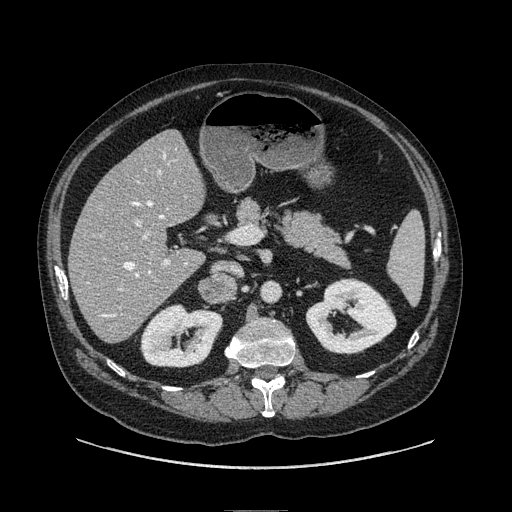
Contrast-enhanced abdominal CT, one axial slice. Slice 36 of 149 in the series (ordered by position). Soft-tissue window (W 400 / L 40 HU). 1.25 mm slice thickness. 512 × 512 image matrix. Male patient. Case-level facts recorded for this patient, not image findings: diagnosis: adrenocortical carcinoma; tumour side: right adrenal; tumour size at pathology: 7.5 cm; Ki-67 index: 15 %; stage (as recorded): 2.
Structures marked on this image (semi-automatically segmented with operator editing):
- mass: box from (x=201, y=276) to (x=233, y=302) px